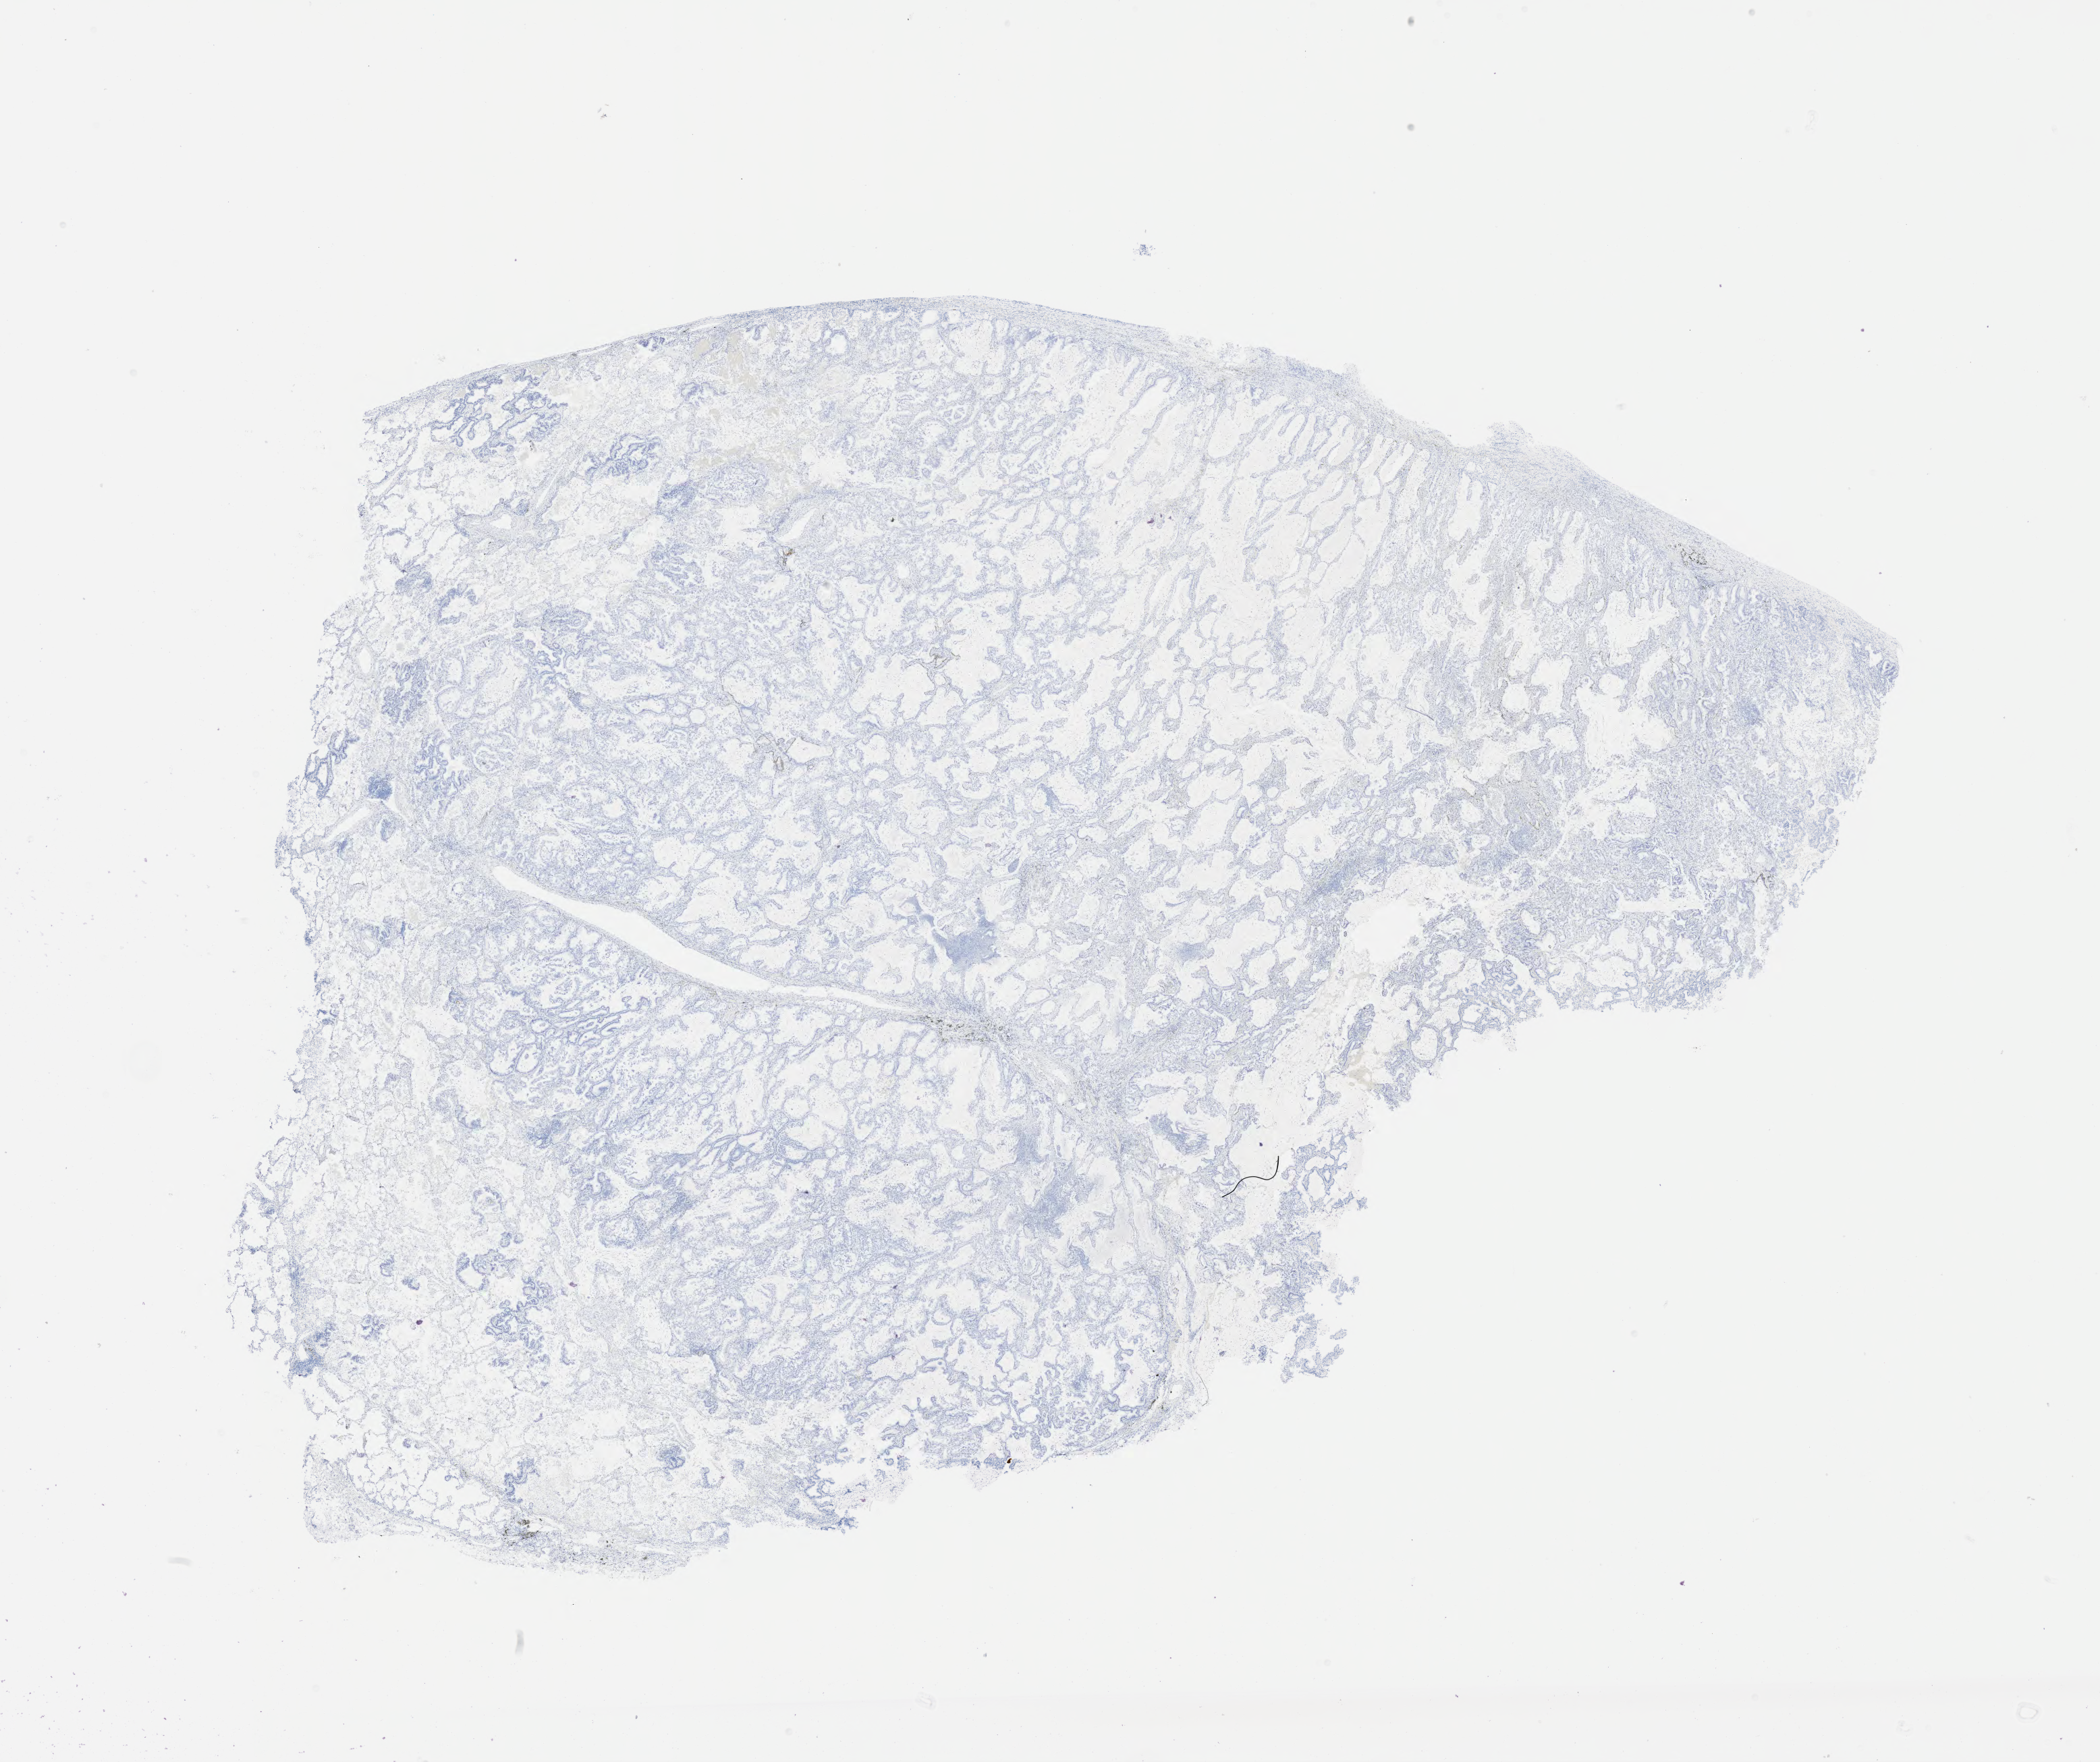
Immunohistochemistry (IHC) whole-slide image stained for p40, whole scanned area (about 25.1 x 21.1 mm) shown as a low-resolution overview. Specimen: tumor tissue. Site: lung. Patient sex: male.
Histologic diagnosis: Adenocarcinoma, NOS.